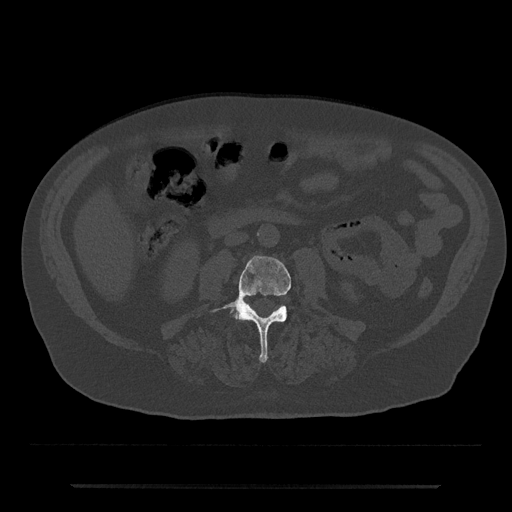
CT including the spine, one axial slice. Reconstruction kernel Br40s/3. 120 kVp. Bone window (W 1800 / L 400 HU). 512 × 512 image matrix, field of view 434 × 434 mm. Male patient, age 80 years. From the clinical record (not read from this slice): primary cancer: prostate; vertebrae with lytic lesions (as recorded): L1, T11.
Outlined on this slice (semi-automatically segmented with operator editing):
- L3 vertebra: bounding box [x1, y1, x2, y2] px = [212, 256, 291, 363]
- L4 vertebra: [233, 312, 237, 319]